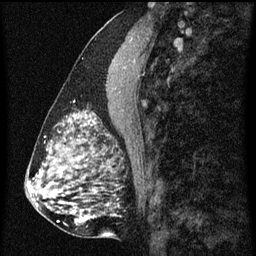
Breast MRI (dynamic contrast-enhanced), one sagittal slice; slice 23 of 60 in the series (ordered by position); dynamic contrast-enhanced series, image 2 of 3 at this slice position (ordered by acquisition); 1.5 T; TE 4.2 ms, TR 8 ms; 2 mm slice thickness; 256 × 256 image matrix. Patient: female, 51 years.
Outlined on this slice (semi-automatic segmentation, software-assisted and operator-edited):
- analysis volume of interest (the breast-tissue region the enhancement analysis was run in; not a lesion): bounding box (x1, y1, x2, y2) in pixels: (61, 112, 102, 129)
- tumour enhancement mask (voxels above the 70 % enhancement threshold inside the analysis volume of interest): (69, 114, 96, 127)